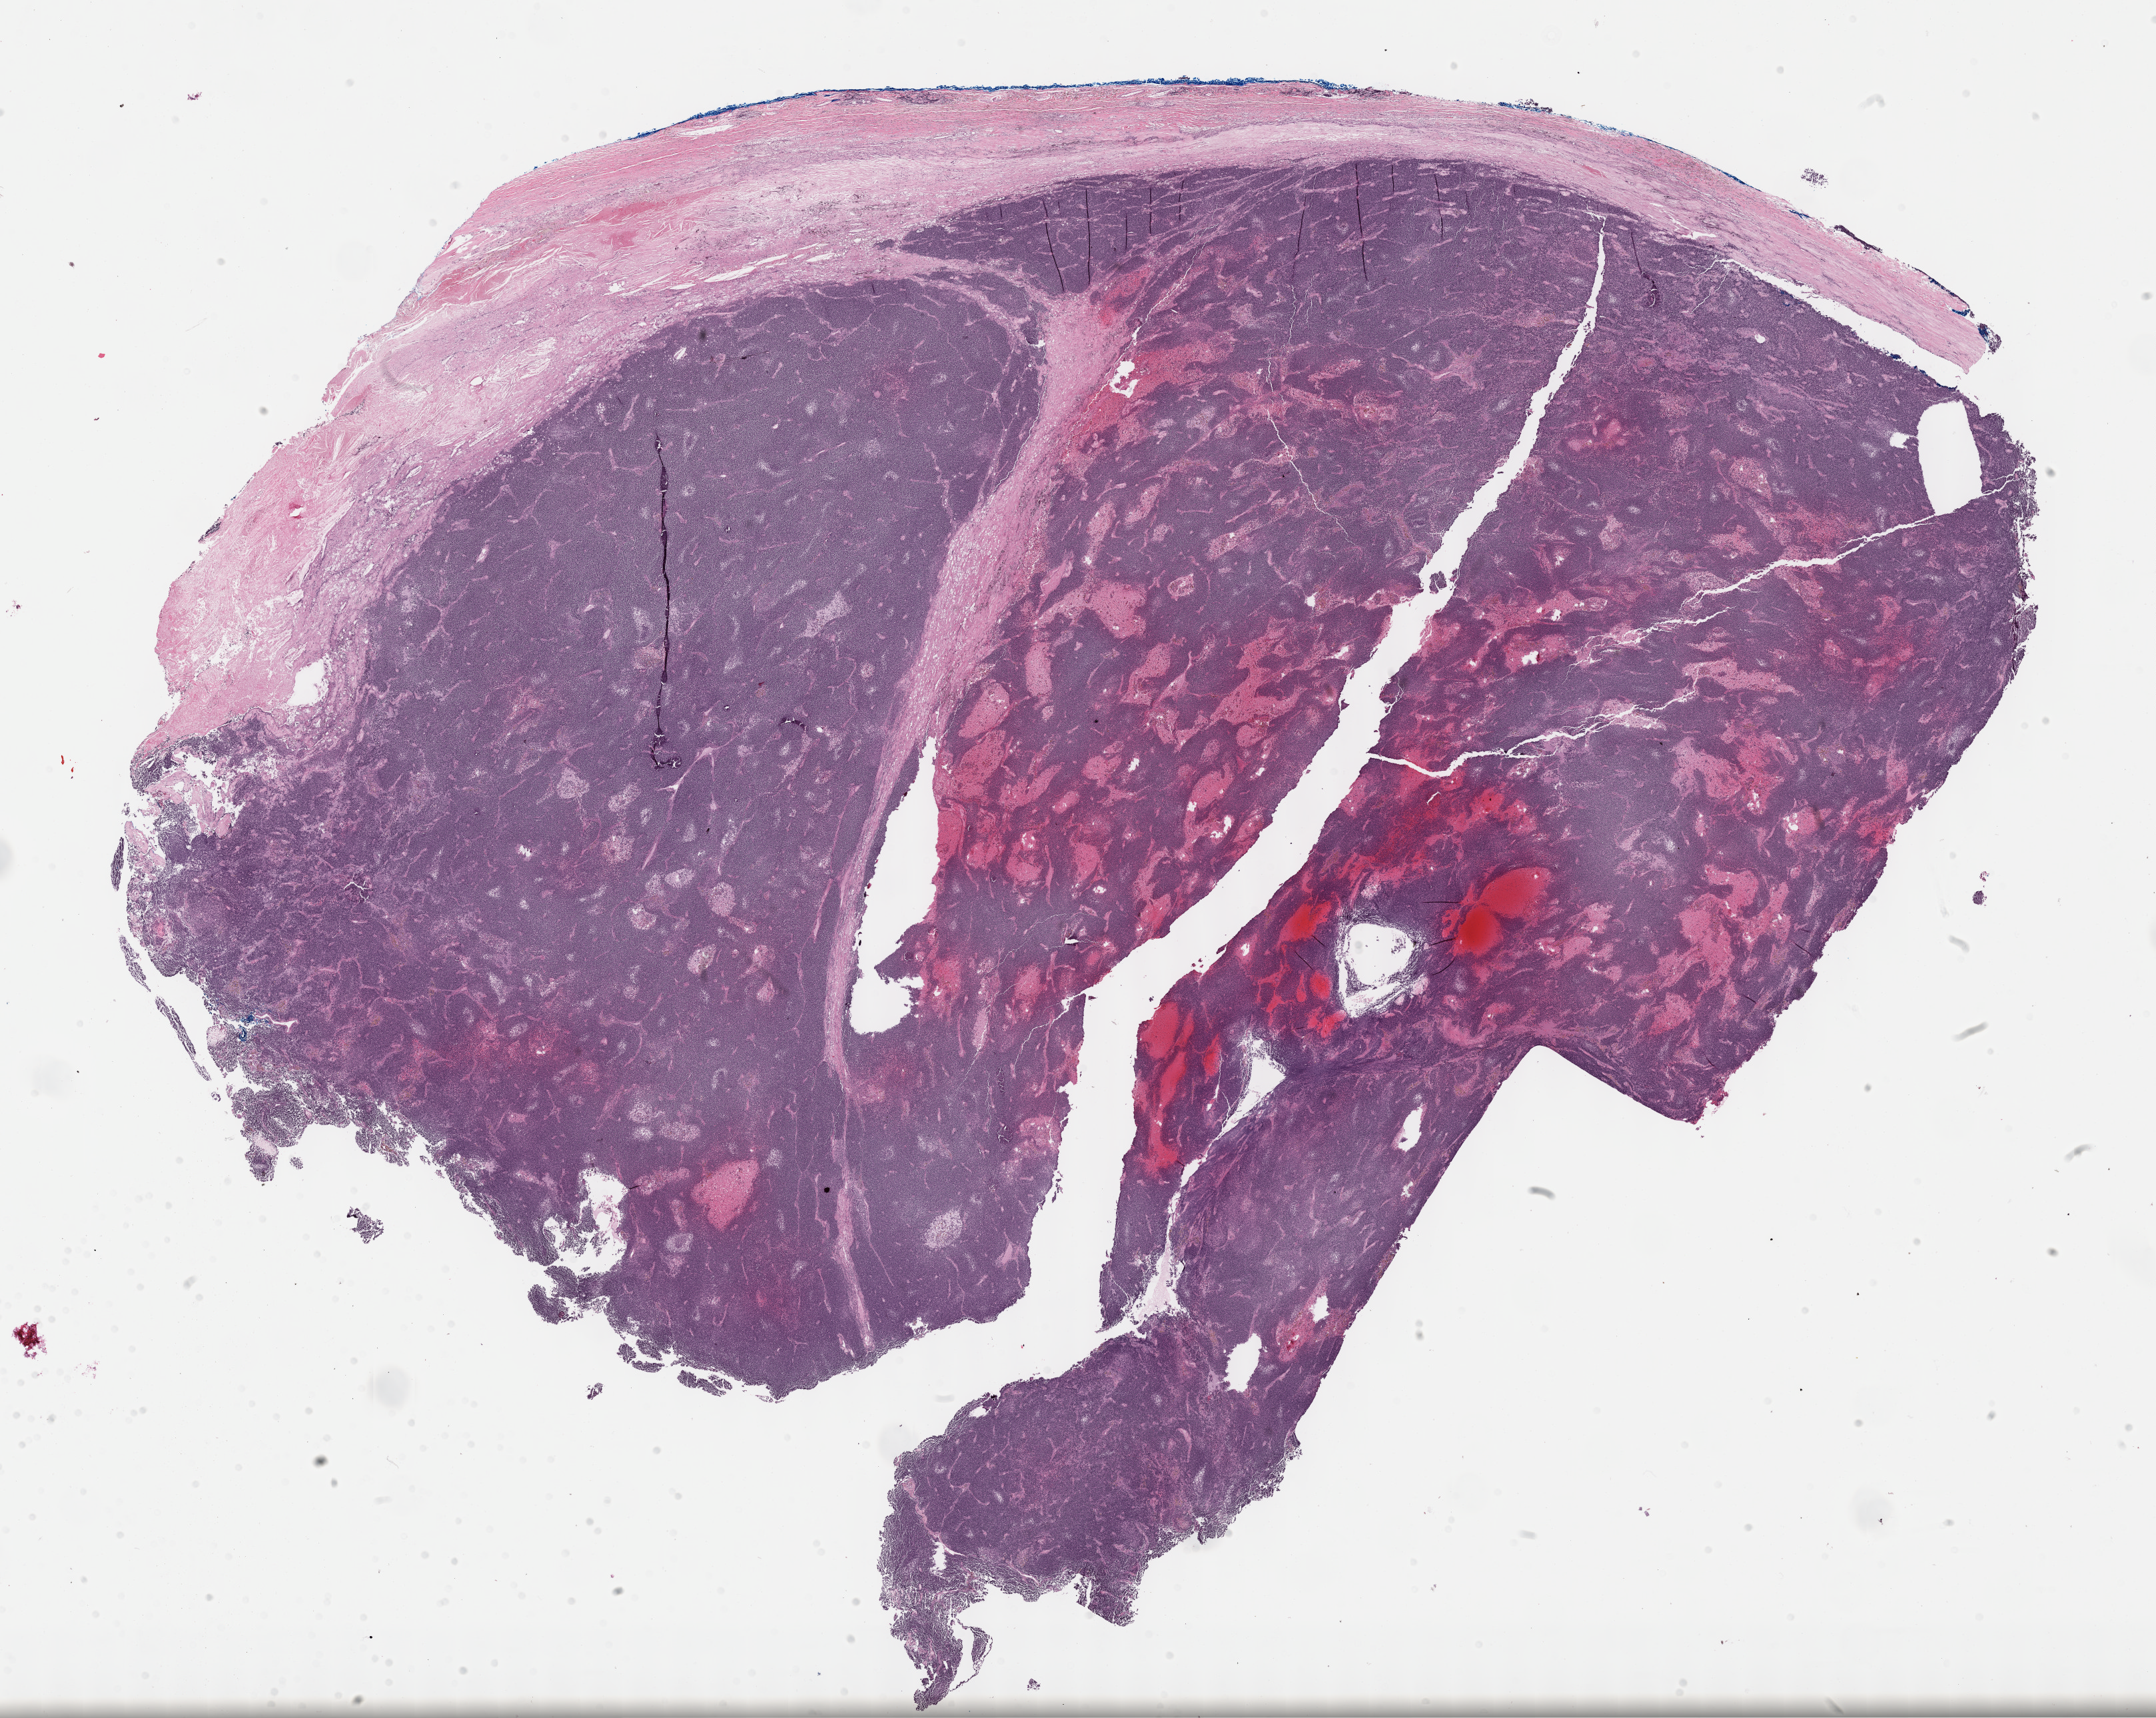
H&E-stained whole-slide image, a low-resolution overview of the entire scanned area, about 26.2 x 20.9 mm (acquisition: 40x scan); formalin-fixed paraffin-embedded (FFPE) diagnostic section; sample: primary tumour, thymus. Patient: female, age at initial diagnosis 68 years.
Pathologic diagnosis: Thymoma, type B1, NOS.